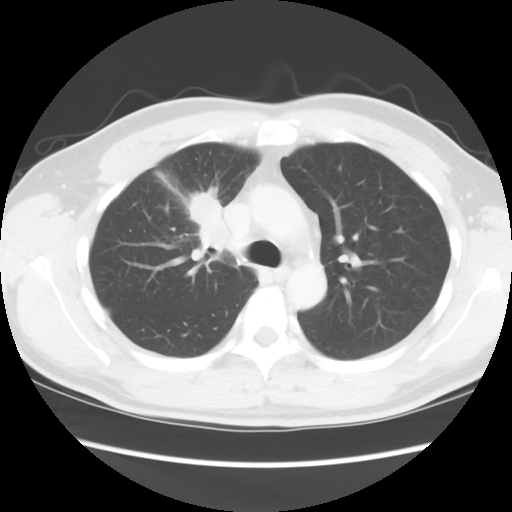
Chest CT, one axial slice. 120 kVp. Lung window (W 1500 / L -600 HU). 5 mm slice thickness. 512 × 512 image matrix, field of view 360 × 360 mm. Male patient, age 35 years. From the clinical record (not read from this slice): clinical TNM (as recorded): T1c N1 M1b.
Structures marked on this image (bounding box drawn by a radiologist):
- lung tumour (recorded histology: adenocarcinoma): bounding box <181,188,229,255> (left, top, right, bottom; pixels)